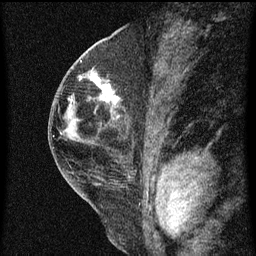
Breast MRI (dynamic contrast-enhanced), one sagittal slice. Position 30 of 60 along the scan axis. Dynamic contrast-enhanced series, image 2 of 3 at this slice position (ordered by acquisition). 1.5 T. TE 4.2 ms, TR 8 ms. 2 mm slice thickness. 256 × 256 image matrix, field of view 180 × 180 mm. Patient: female, 48 years.
Annotated regions visible in this slice (semi-automatically segmented with operator editing):
- analysis volume of interest (the breast-tissue region the enhancement analysis was run in; not a lesion): bounding box <89,72,120,113> (left, top, right, bottom; pixels)
- tumour enhancement mask (voxels above the 70 % enhancement threshold inside the analysis volume of interest): <92,76,119,103>